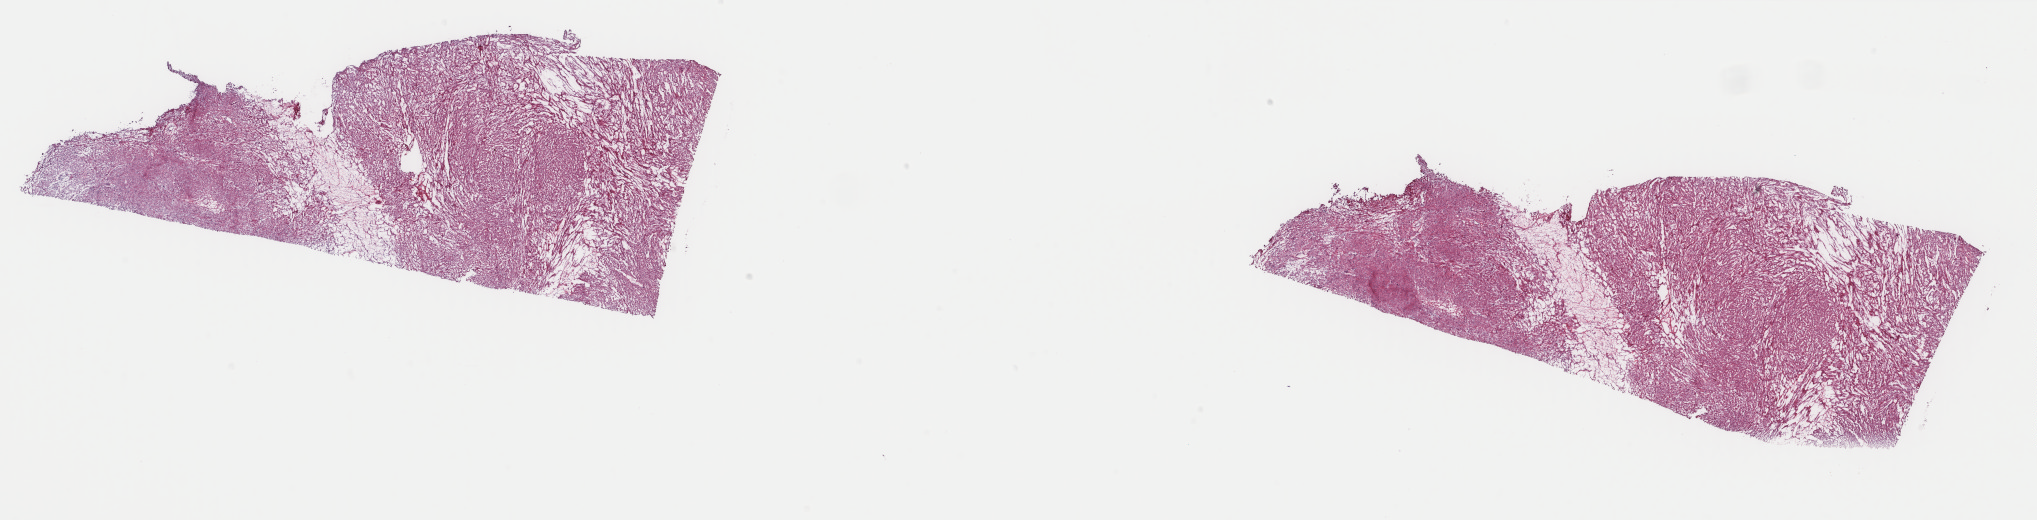
Digitized H&E tissue section (whole slide) — whole scanned area (about 32.3 x 8.3 mm) shown as a low-resolution overview, frozen section, sample: primary tumour, connective, subcutaneous and other soft tissues. Patient: female, age at initial diagnosis 45 years. Slide review estimates, as recorded: tumour cells 95%, tumour nuclei 95%.
Pathologic diagnosis: Leiomyosarcoma, NOS (overlapping lesion of connective, subcutaneous and other soft tissues).